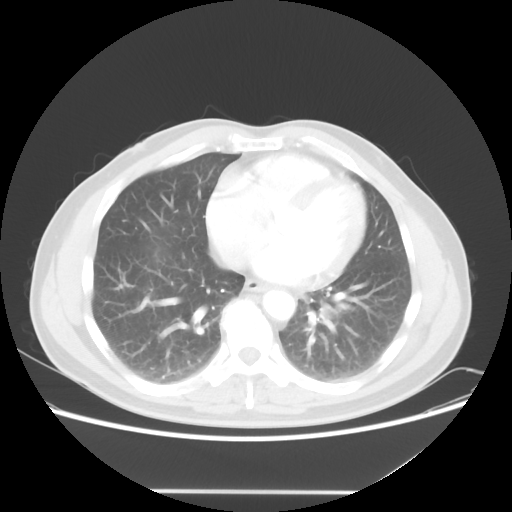
Chest CT, one axial slice. Slice 23 of 56 in the series (ordered by position). 120 kVp. Lung window (W 1500 / L -600 HU). 5 mm slice thickness. 512 × 512 image matrix, field of view 385 × 385 mm. Patient: male, 61 years. Case-level facts recorded for this patient, not image findings: clinical TNM (as recorded): T1c N0 M0; histopathological grade: G3.
Structures marked on this image (bounding box drawn by a radiologist):
- lung tumour (recorded histology: adenocarcinoma): bounding box <313,297,345,330> (left, top, right, bottom; pixels)